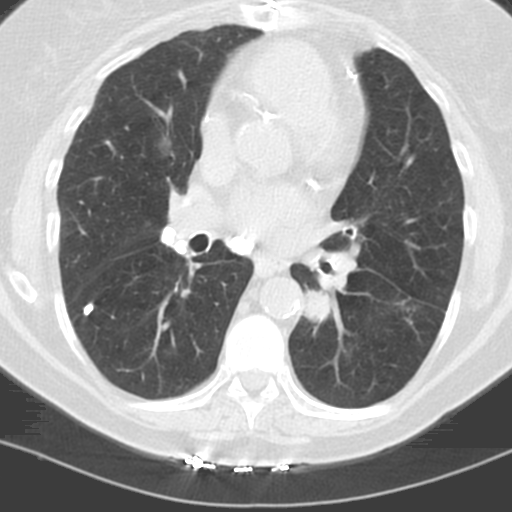
Low-dose screening chest CT, one axial slice. Position 57 of 121 along the scan axis. Lung window (W 1500 / L -600 HU). 3.2 mm slice thickness. 512 × 512 image matrix, field of view 278 × 278 mm.
Structures marked on this image (outlined manually by an expert reader):
- lesion 2 (tumor, lower lobe of left lung): bounding box (x1, y1, x2, y2) in pixels: (305, 290, 332, 323)